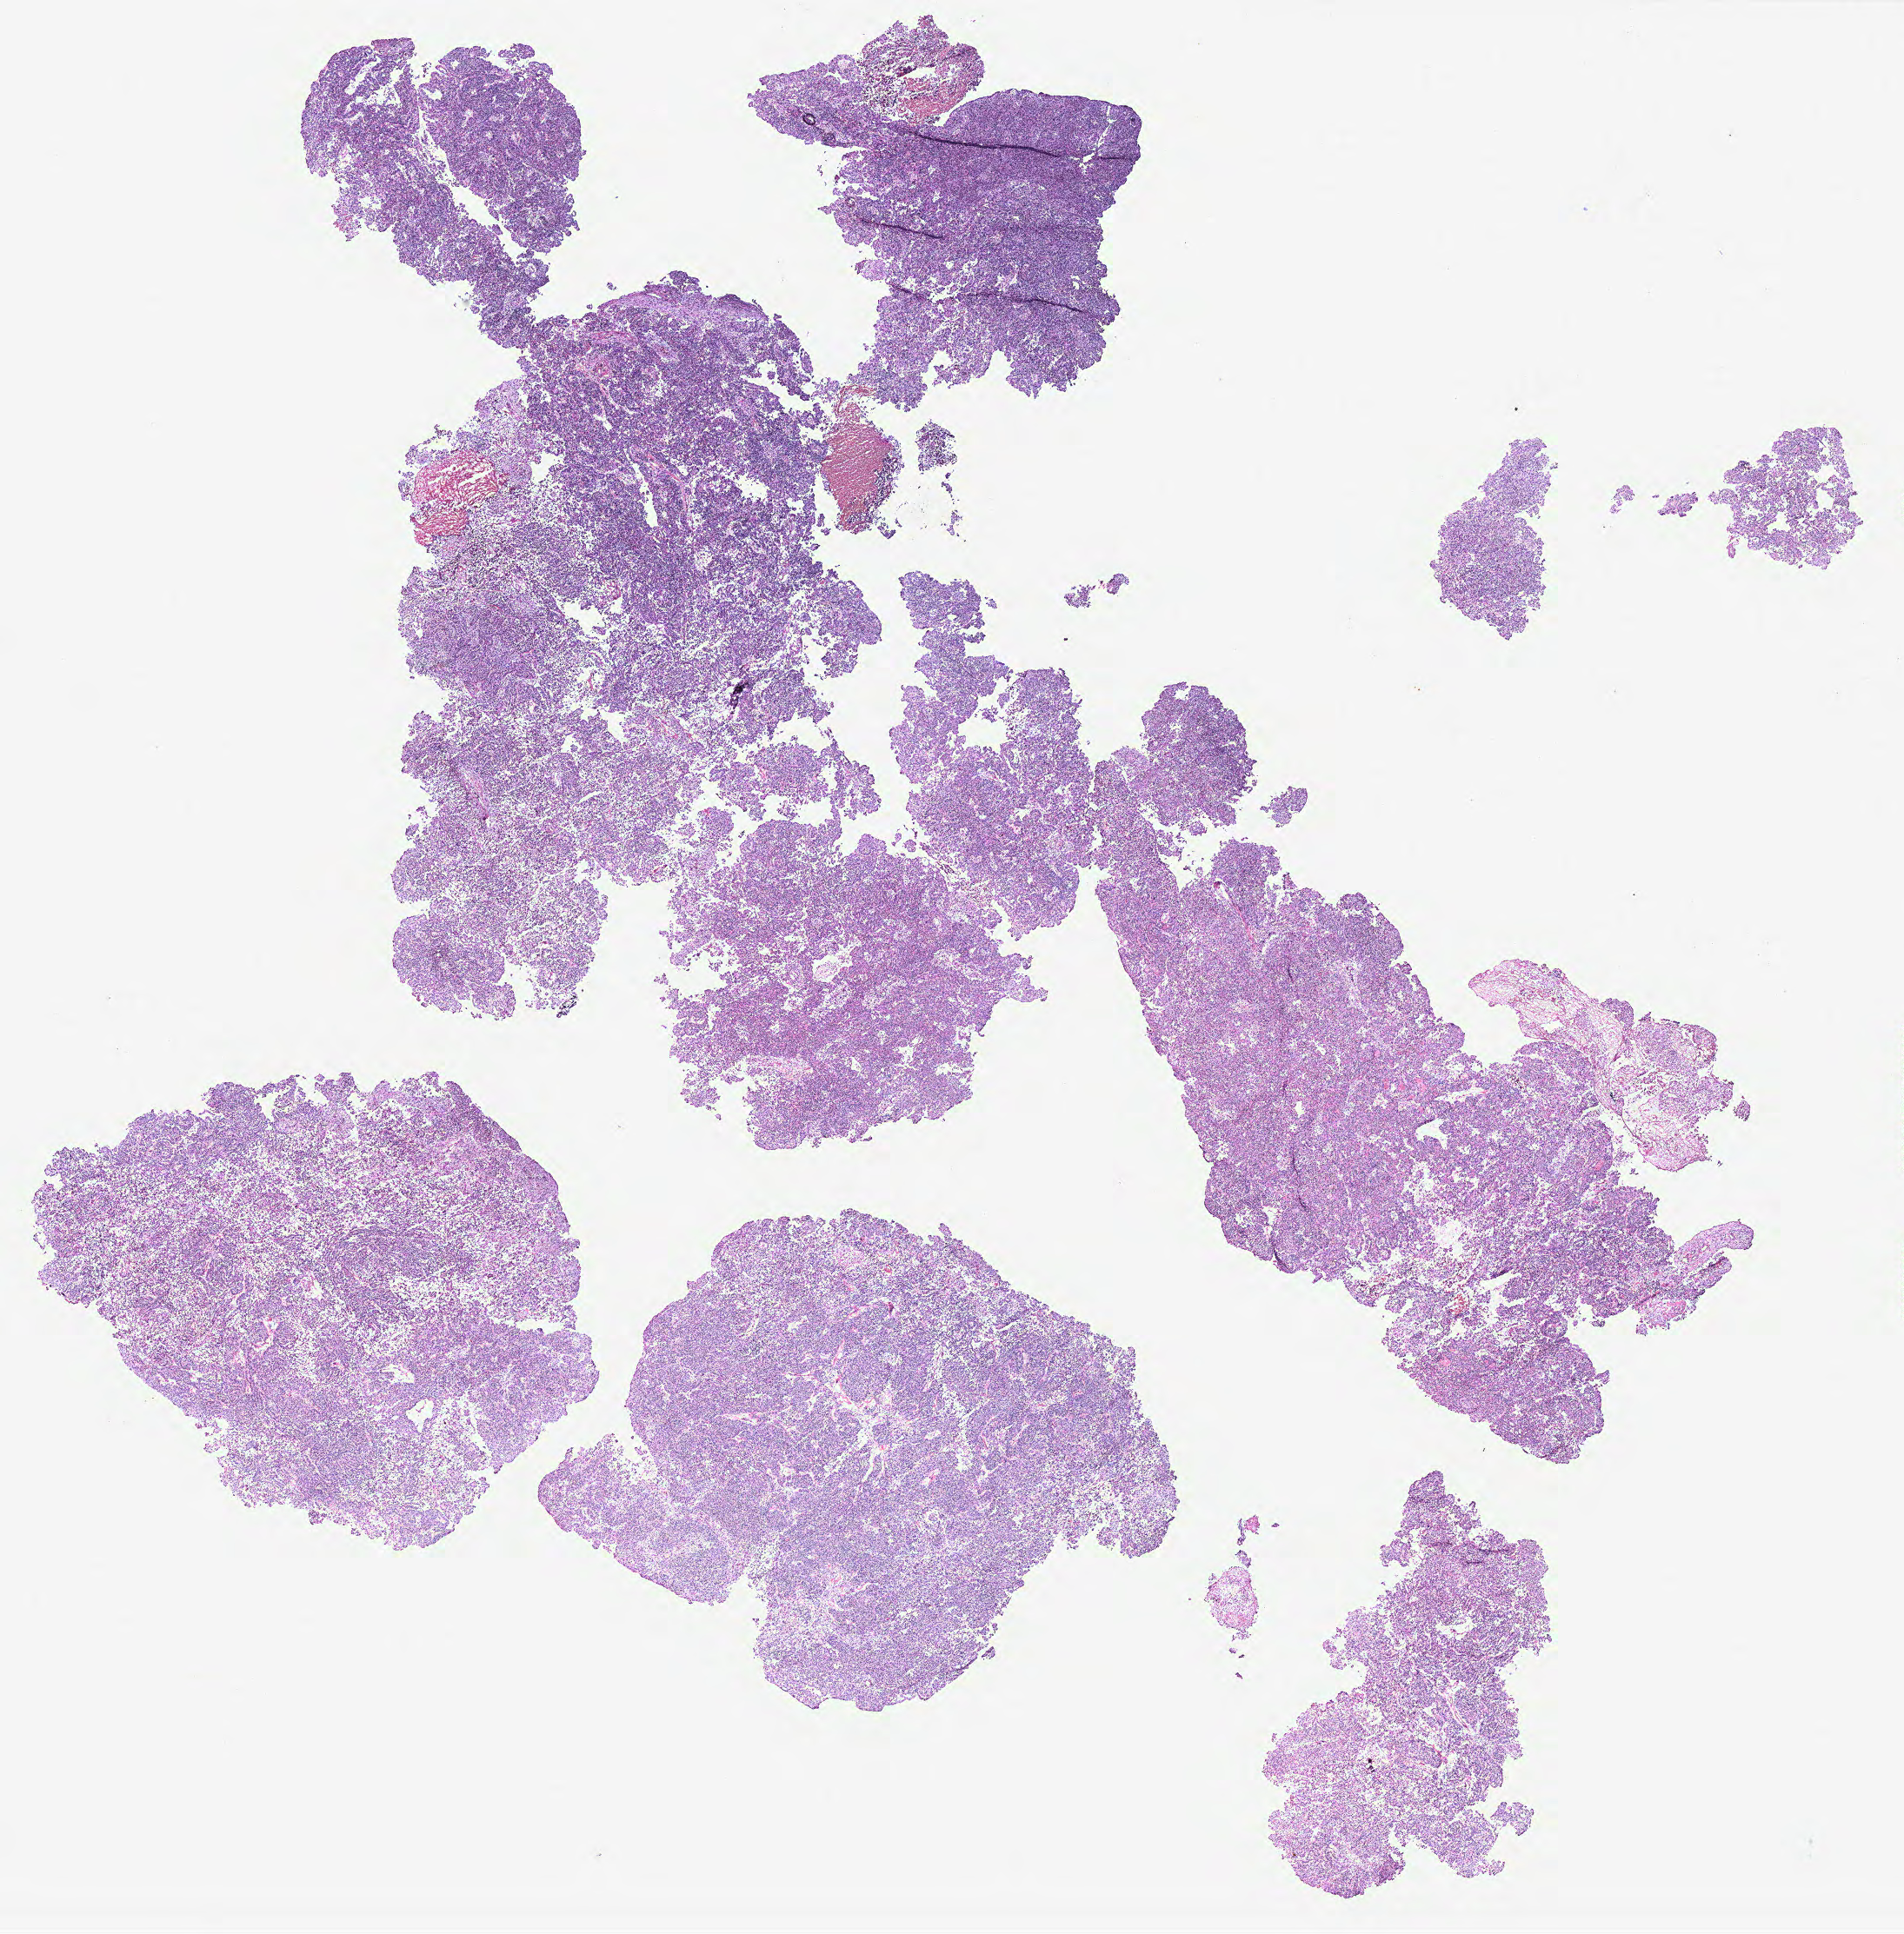
Hematoxylin and eosin (H&E) stained whole-slide image, shown as a low-resolution overview of the whole scanned area (about 17.5 x 17.8 mm, from a 40x scan), tumour tissue sample, ovary. Female, 79 y/o.
Primary tumour site (as recorded): ovary. Diagnosis: Serous adenocarcinoma, NOS.